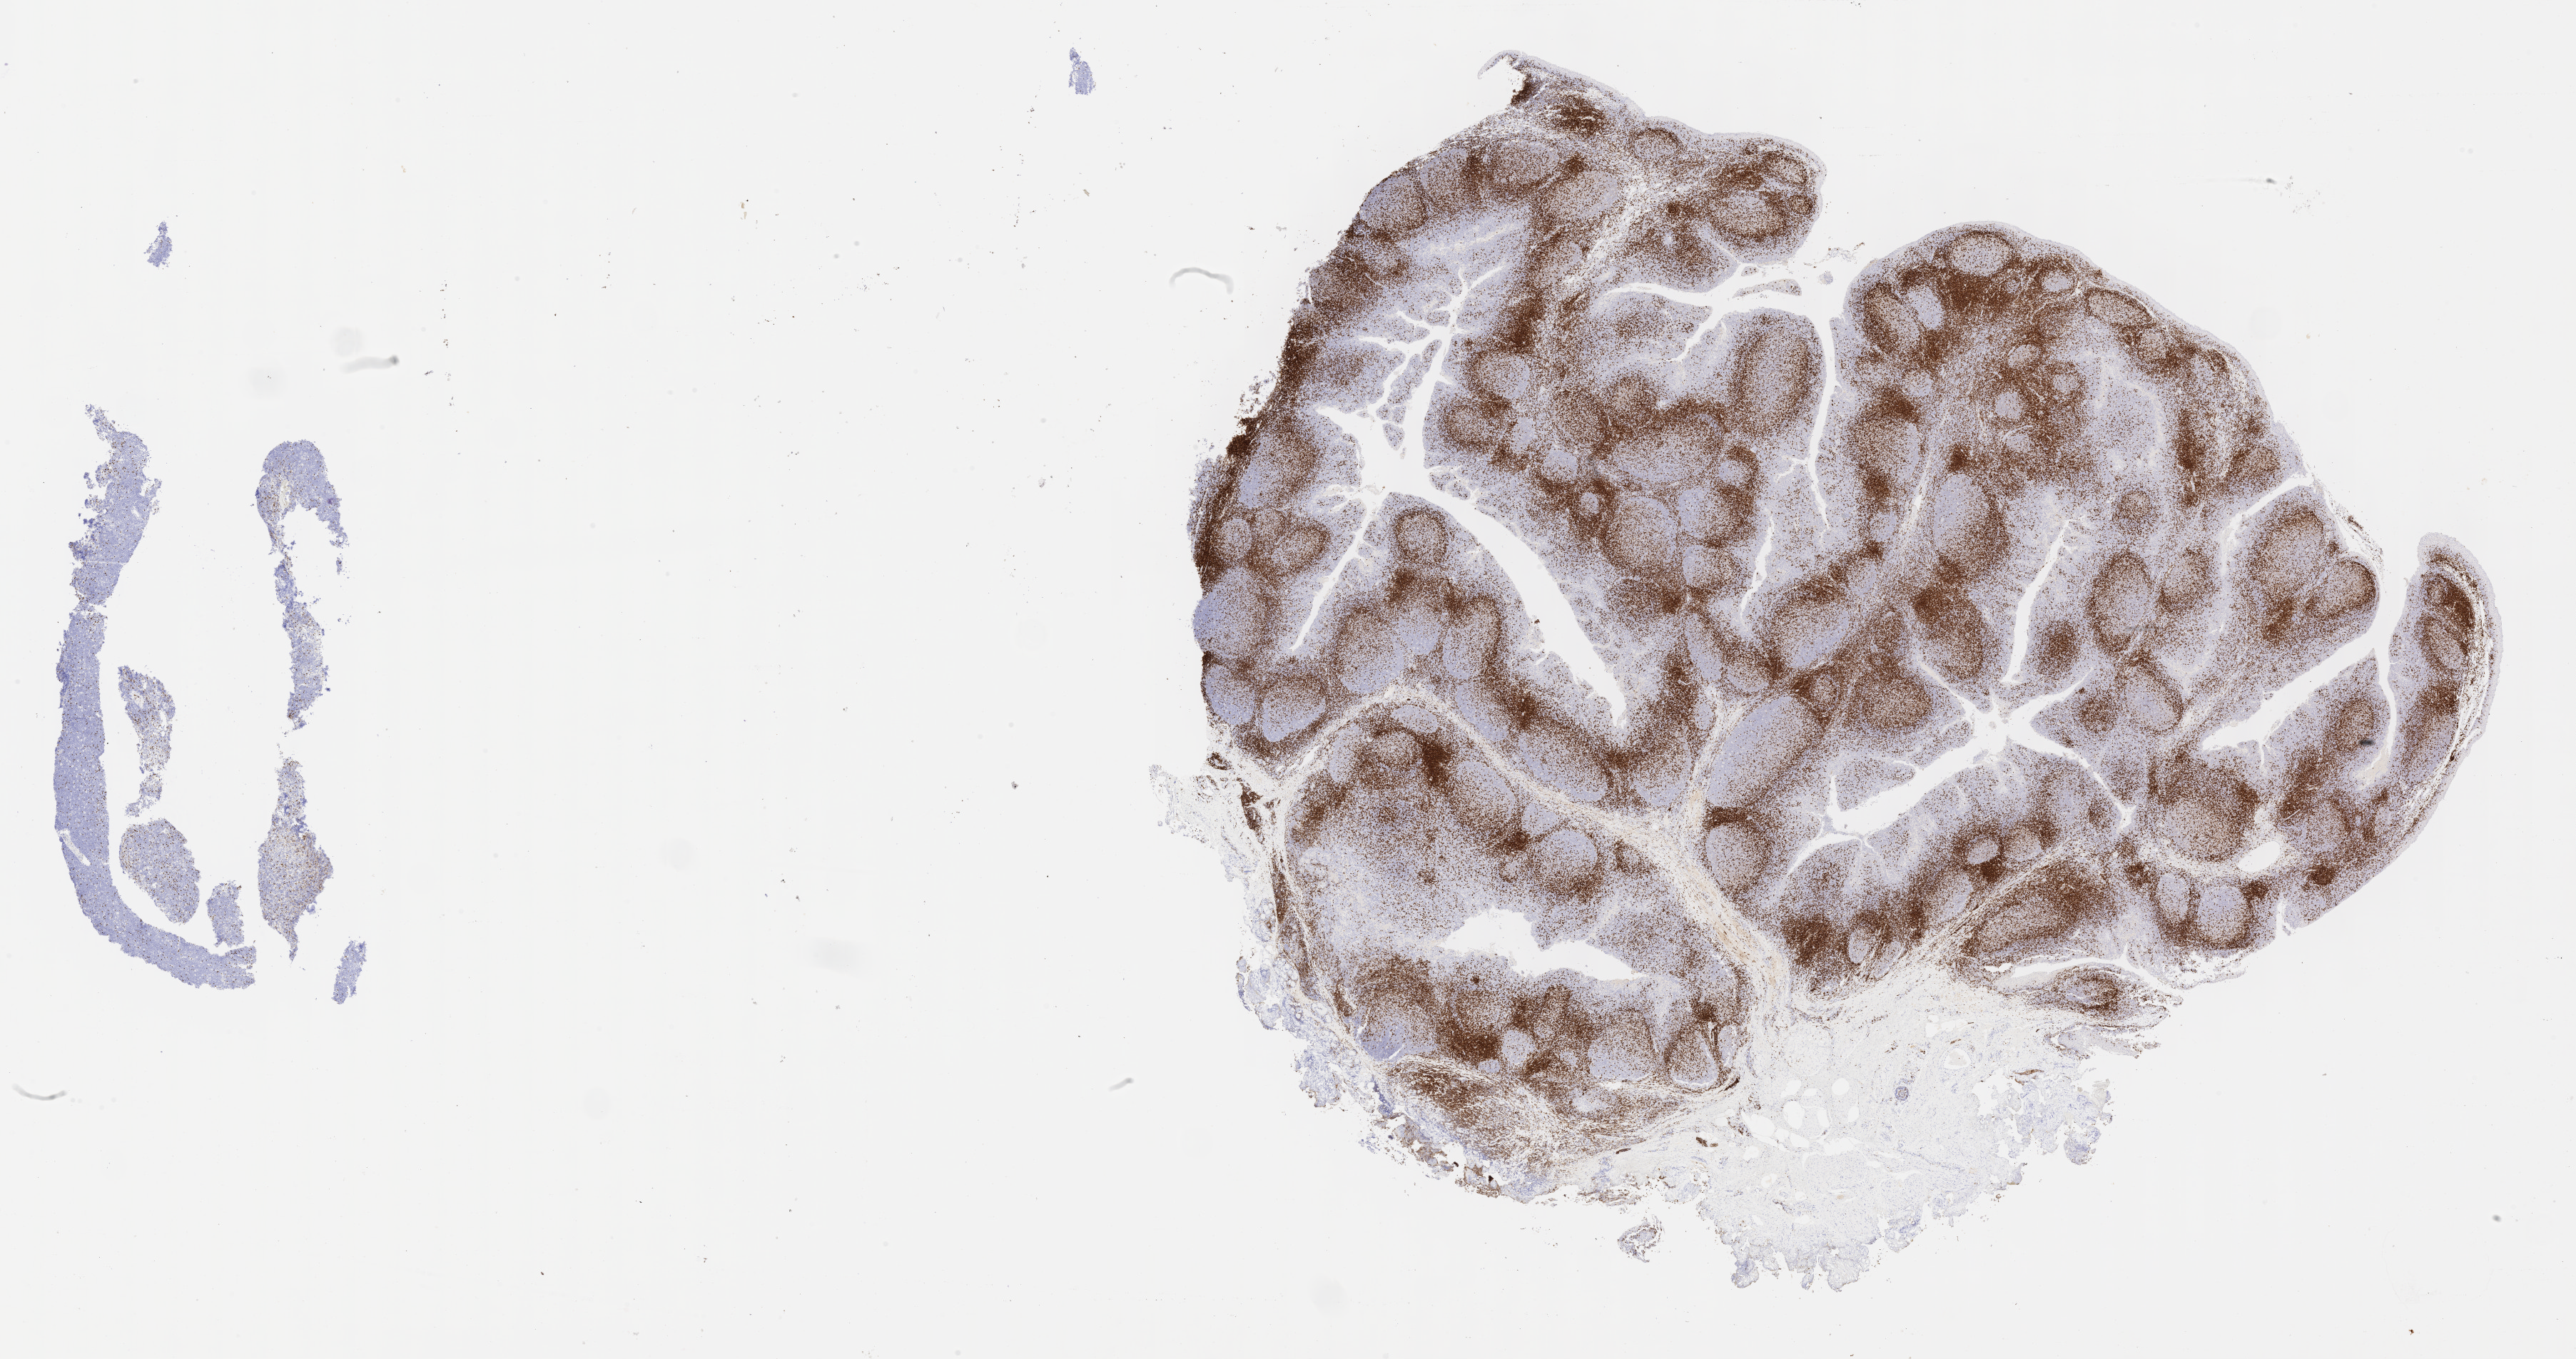
Whole-slide image, immunohistochemical stain for CD3, whole scanned area (about 29.2 x 15.4 mm) shown as a low-resolution overview, specimen: tumor tissue. Patient: female, aged 10.
Histologic diagnosis: Burkitt lymphoma, NOS.